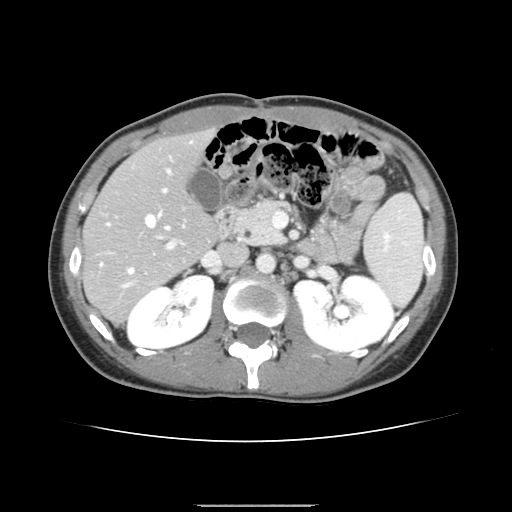
Contrast-enhanced abdominal CT, one axial slice. Slice 79 of 150 in the series (ordered by position). 120 kVp. Intravenous contrast given. Soft-tissue window (W 400 / L 40 HU). 2.5 mm slice thickness. 512 × 512 image matrix, field of view 324 × 324 mm. Female patient, age 32 years. From the clinical record (not read from this slice): diagnosis: colorectal cancer liver metastases, imaged before liver resection; multiple liver metastases: yes; largest metastasis: 0.7 cm; disease in both lobes: no.
Structures marked on this image (manually delineated by an expert):
- hepatic veins: bounding box [x1, y1, x2, y2] px = [100, 213, 169, 273]
- liver: [85, 132, 217, 321]
- planned liver remnant (the part of the liver to remain after resection): [86, 132, 217, 278]
- portal vein (with intrahepatic branches): [107, 157, 174, 287]